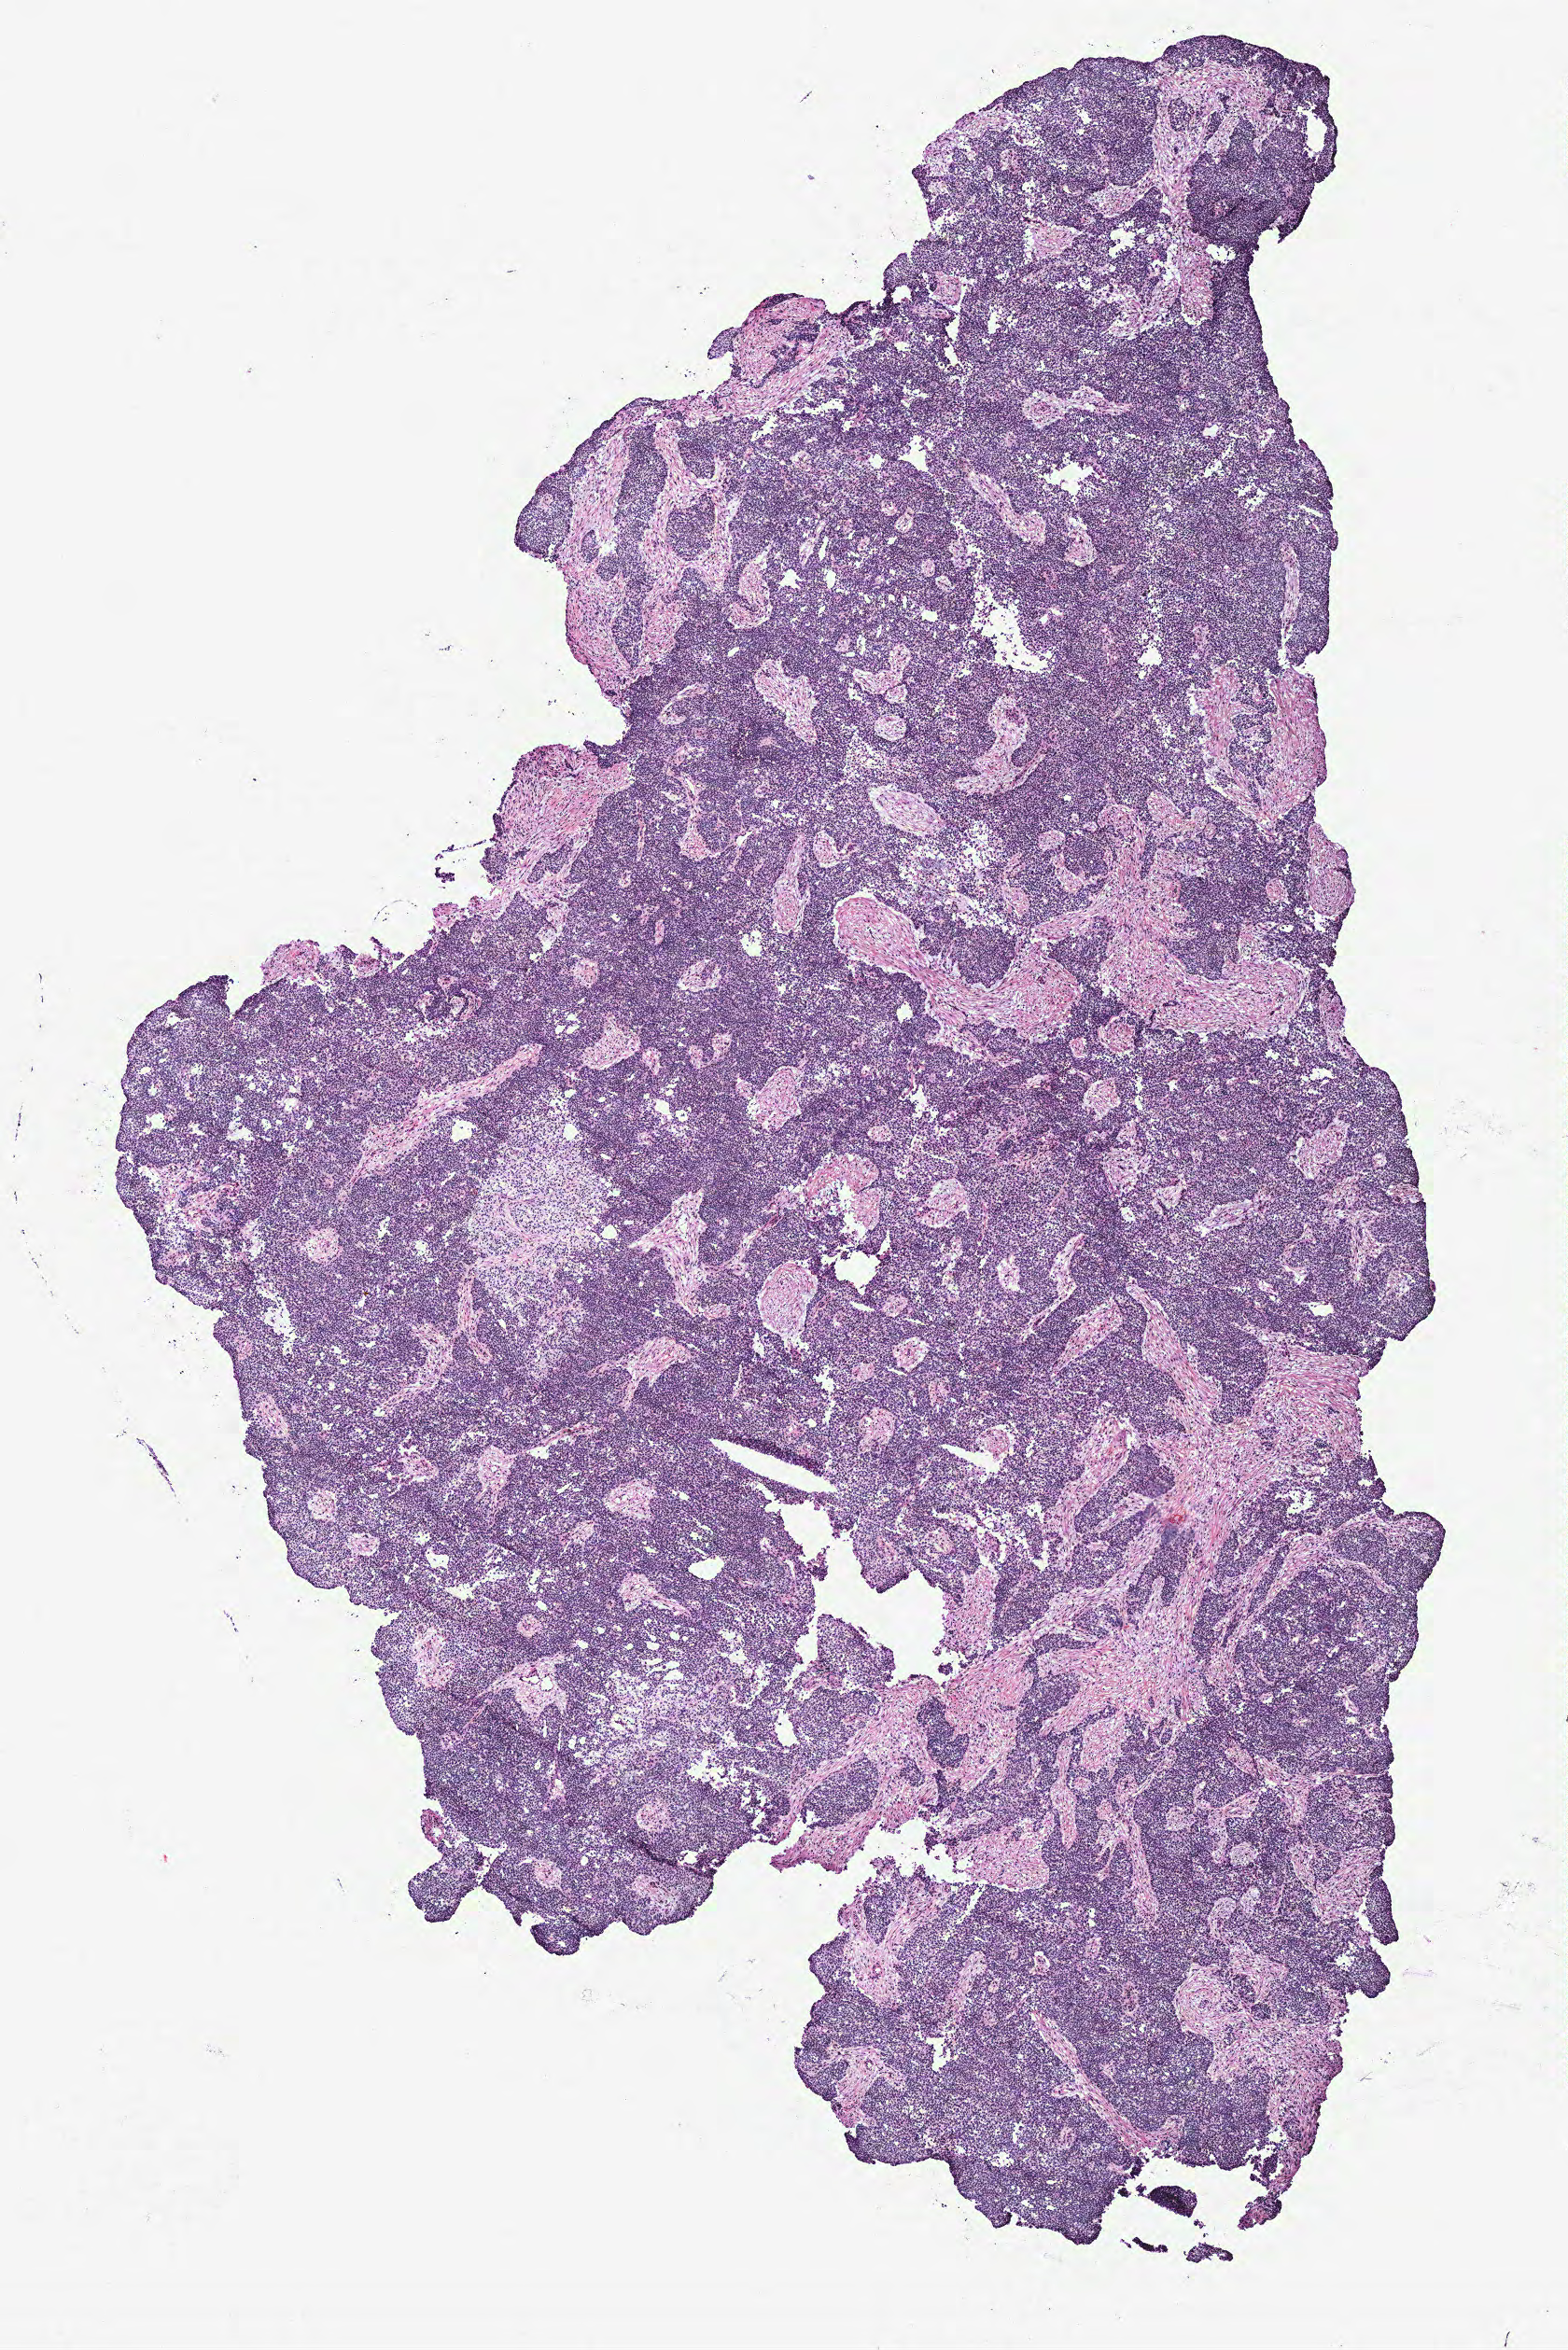
Whole-slide histology image, H&E, a low-resolution overview of the entire scanned area, about 6.7 x 10.1 mm, ovary, tumour tissue. 48-year-old female patient.
Primary tumour site (as recorded): ovary. Diagnosis: Serous adenocarcinoma, NOS.